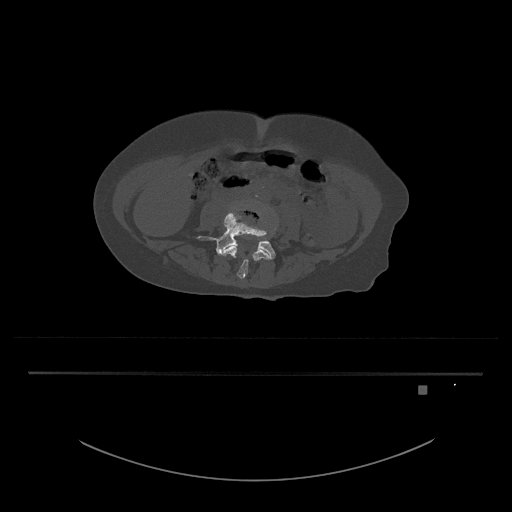
CT including the spine, one axial slice. Slice 331 of 797 in the series (ordered by position). Reconstruction kernel Br40s/3. 120 kVp. Bone window (W 1800 / L 400 HU). 0.5 mm slice thickness. 512 × 512 image matrix, field of view 500 × 500 mm. Patient: female, 57 years. Case-level facts recorded for this patient, not image findings: primary cancer: cervical.
Structures marked on this image (semi-automatic segmentation, software-assisted and operator-edited):
- L4 vertebra: bounding box <221,208,272,279> (left, top, right, bottom; pixels)